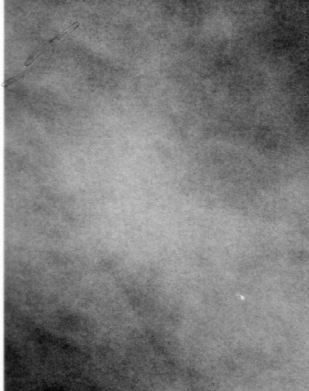
Region of interest cut from a scanned film mammogram (one marked finding), left breast, CC view, BI-RADS breast density category 3 (scale 1–4).
Finding: mass, shape irregular / architectural distortion, margins ill defined / spiculated; BI-RADS assessment category 4; subtlety rating 4 on a 1 (subtle) to 5 (obvious) scale; pathology result (as recorded, not read from the image): malignant.